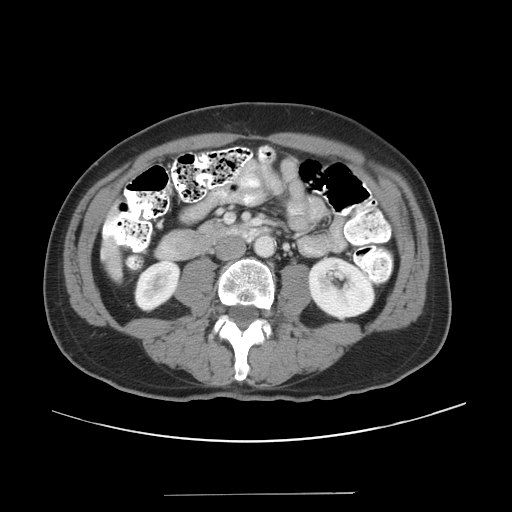
Contrast-enhanced abdominal CT, one axial slice; position 8 of 43 along the scan axis; reconstruction kernel STANDARD; 120 kVp; intravenous contrast given; soft-tissue window (W 400 / L 40 HU); 5 mm slice thickness; 512 × 512 image matrix, field of view 409 × 409 mm. Male patient, age 65 years. From the clinical record (not read from this slice): diagnosis: colorectal cancer liver metastases, imaged before liver resection; multiple liver metastases: no; largest metastasis: 3.8 cm; chemotherapy before resection: yes.
Annotated regions visible in this slice (expert manual segmentation):
- liver: bounding box (x1, y1, x2, y2) in pixels: (110, 260, 116, 272)
- planned liver remnant (the part of the liver to remain after resection): (110, 260, 116, 272)